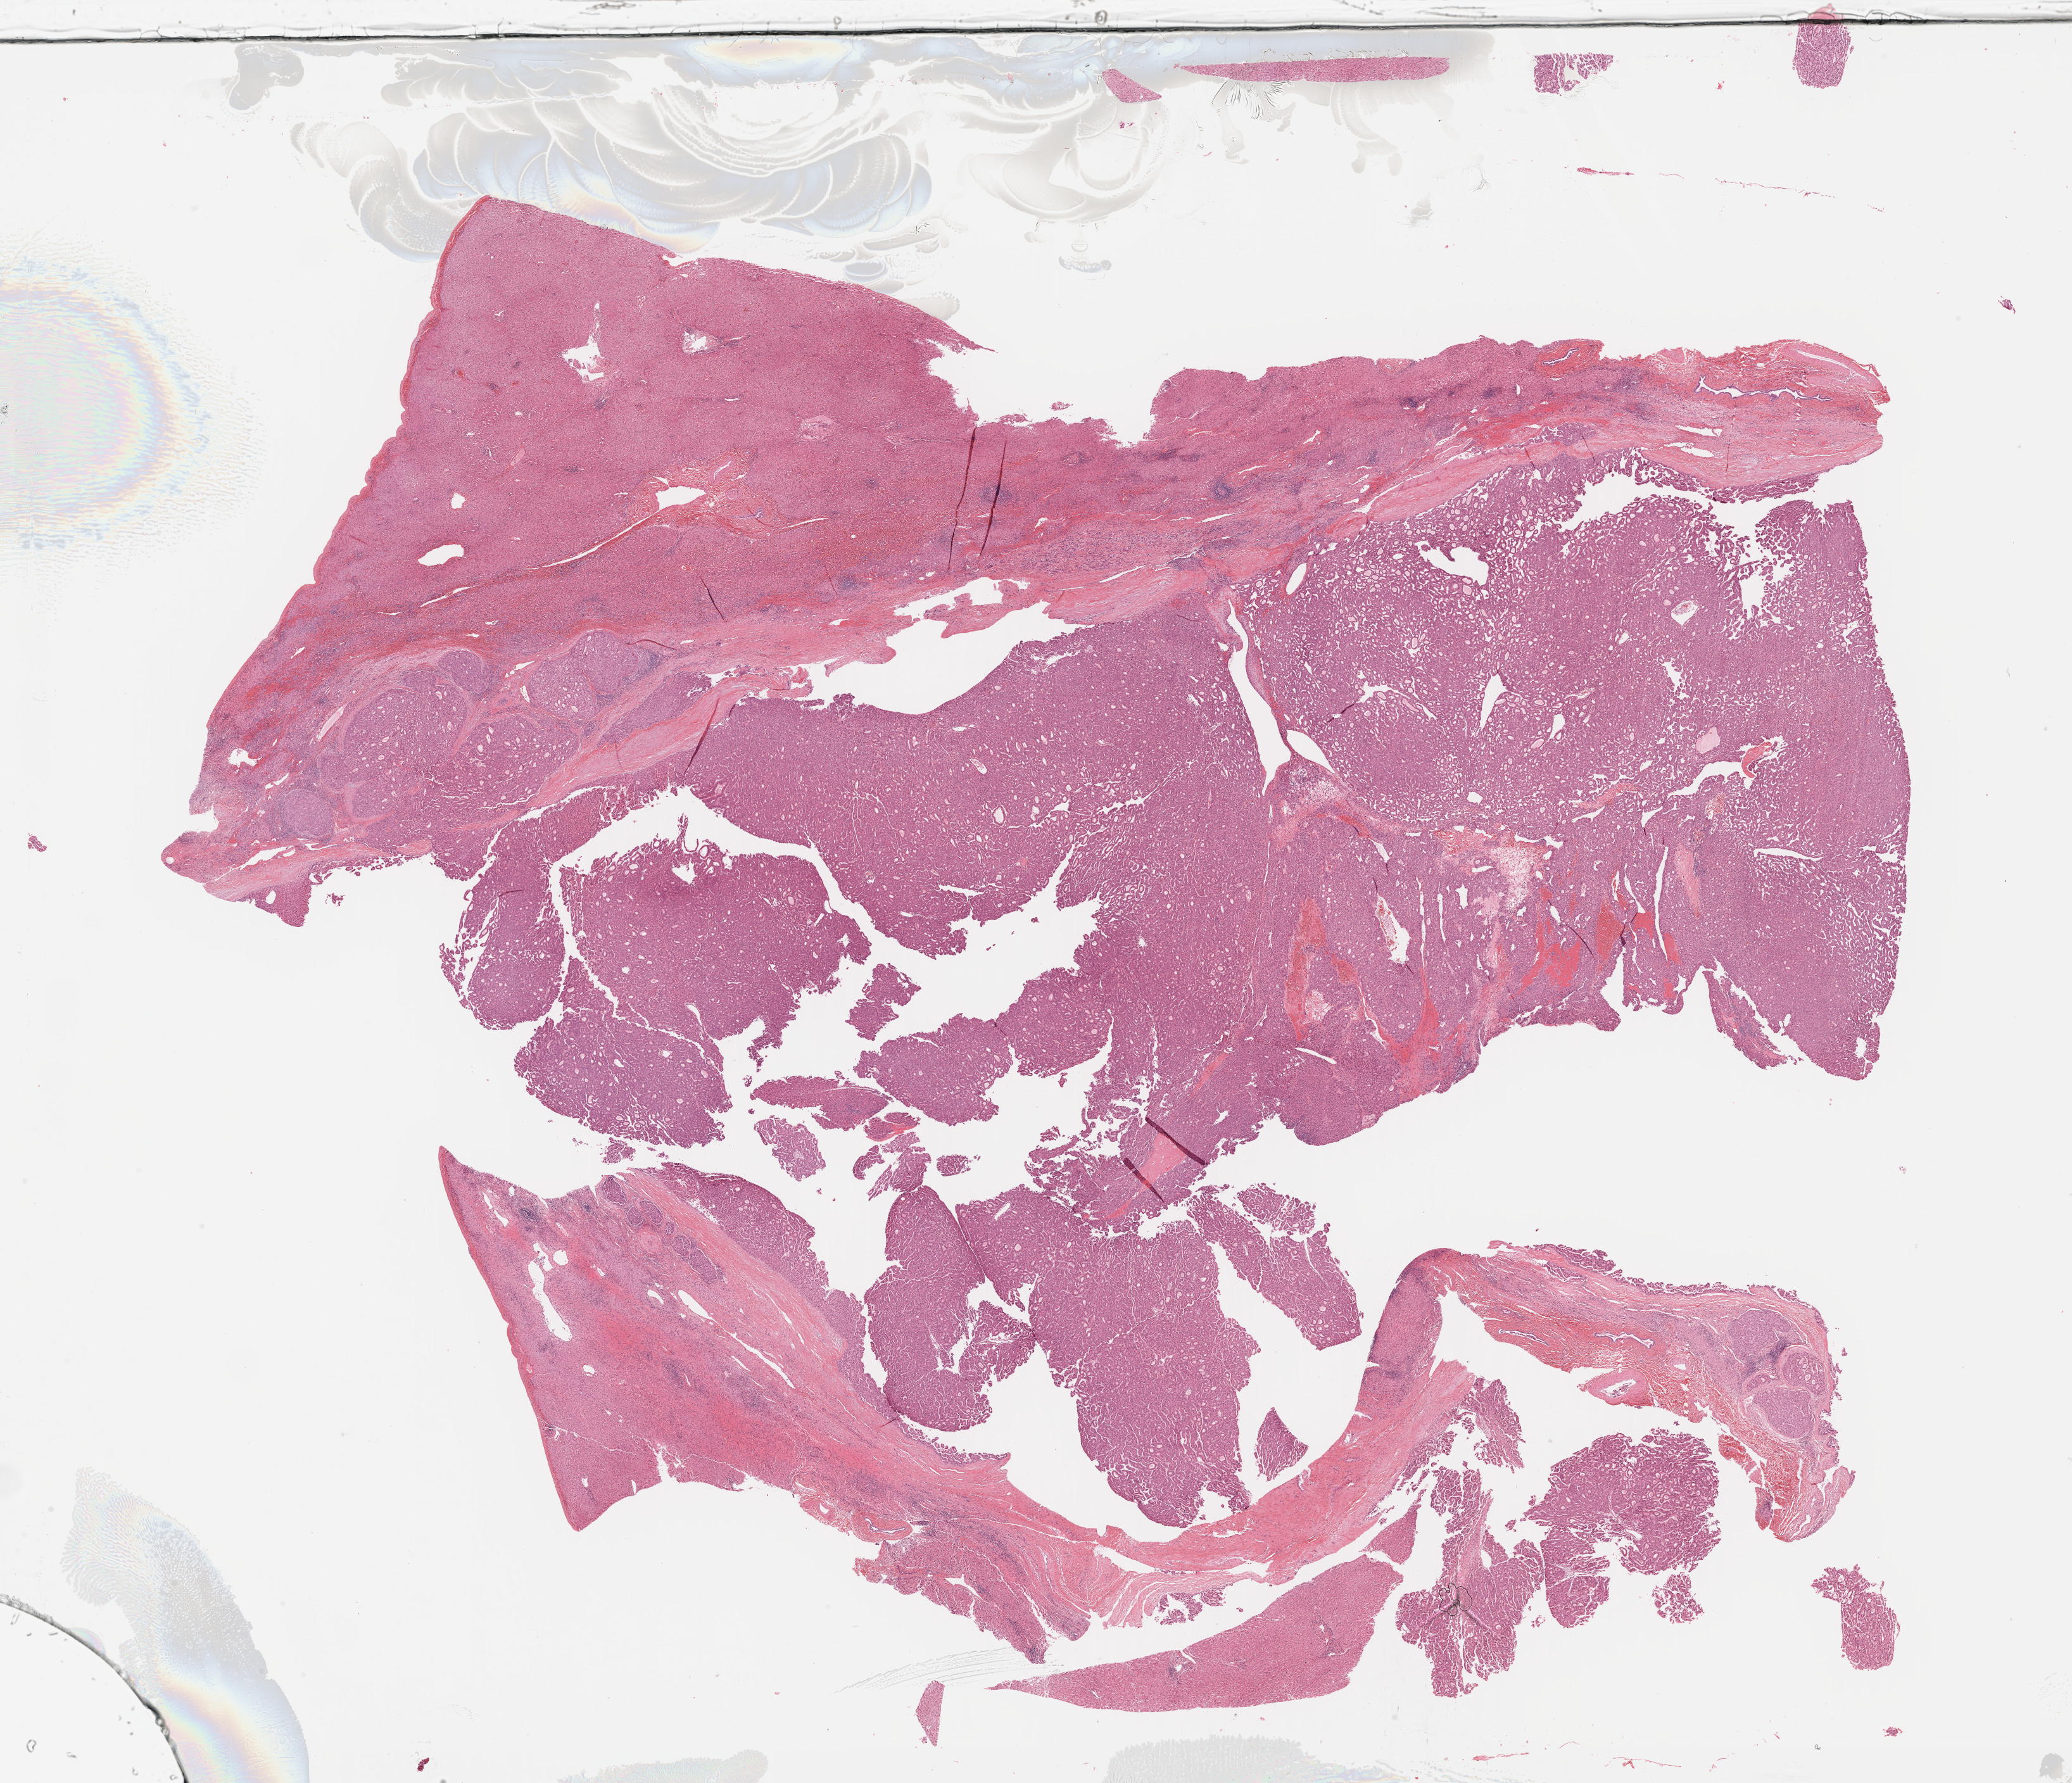
Whole-slide histology image, Hematoxylin and eosin (H&E) stained — shown as a low-resolution overview of the whole scanned area (about 26.5 x 22.8 mm), formalin-fixed paraffin-embedded (FFPE) diagnostic section, sample: primary tumour, liver. Male patient; age at initial diagnosis 68 years. Histologic grade: G2 (moderately differentiated).
Histologic diagnosis: Hepatocellular carcinoma, NOS. AJCC pathologic stage: II (5th edition).